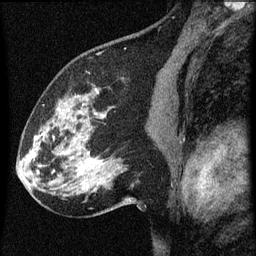
Breast MRI (dynamic contrast-enhanced), one sagittal slice; position 39 of 60 along the scan axis; dynamic contrast-enhanced series, image 2 of 3 at this slice position (ordered by acquisition); 1.5 T; TE 4.2 ms, TR 8 ms; 2 mm slice thickness; 256 × 256 image matrix, field of view 180 × 180 mm. Female patient, age 61 years.
Outlined on this slice (semi-automatically segmented with operator editing):
- analysis volume of interest (the breast-tissue region the enhancement analysis was run in; not a lesion): bounding box [x1, y1, x2, y2] px = [27, 80, 139, 209]
- tumour enhancement mask (voxels above the 70 % enhancement threshold inside the analysis volume of interest): [33, 90, 98, 159]